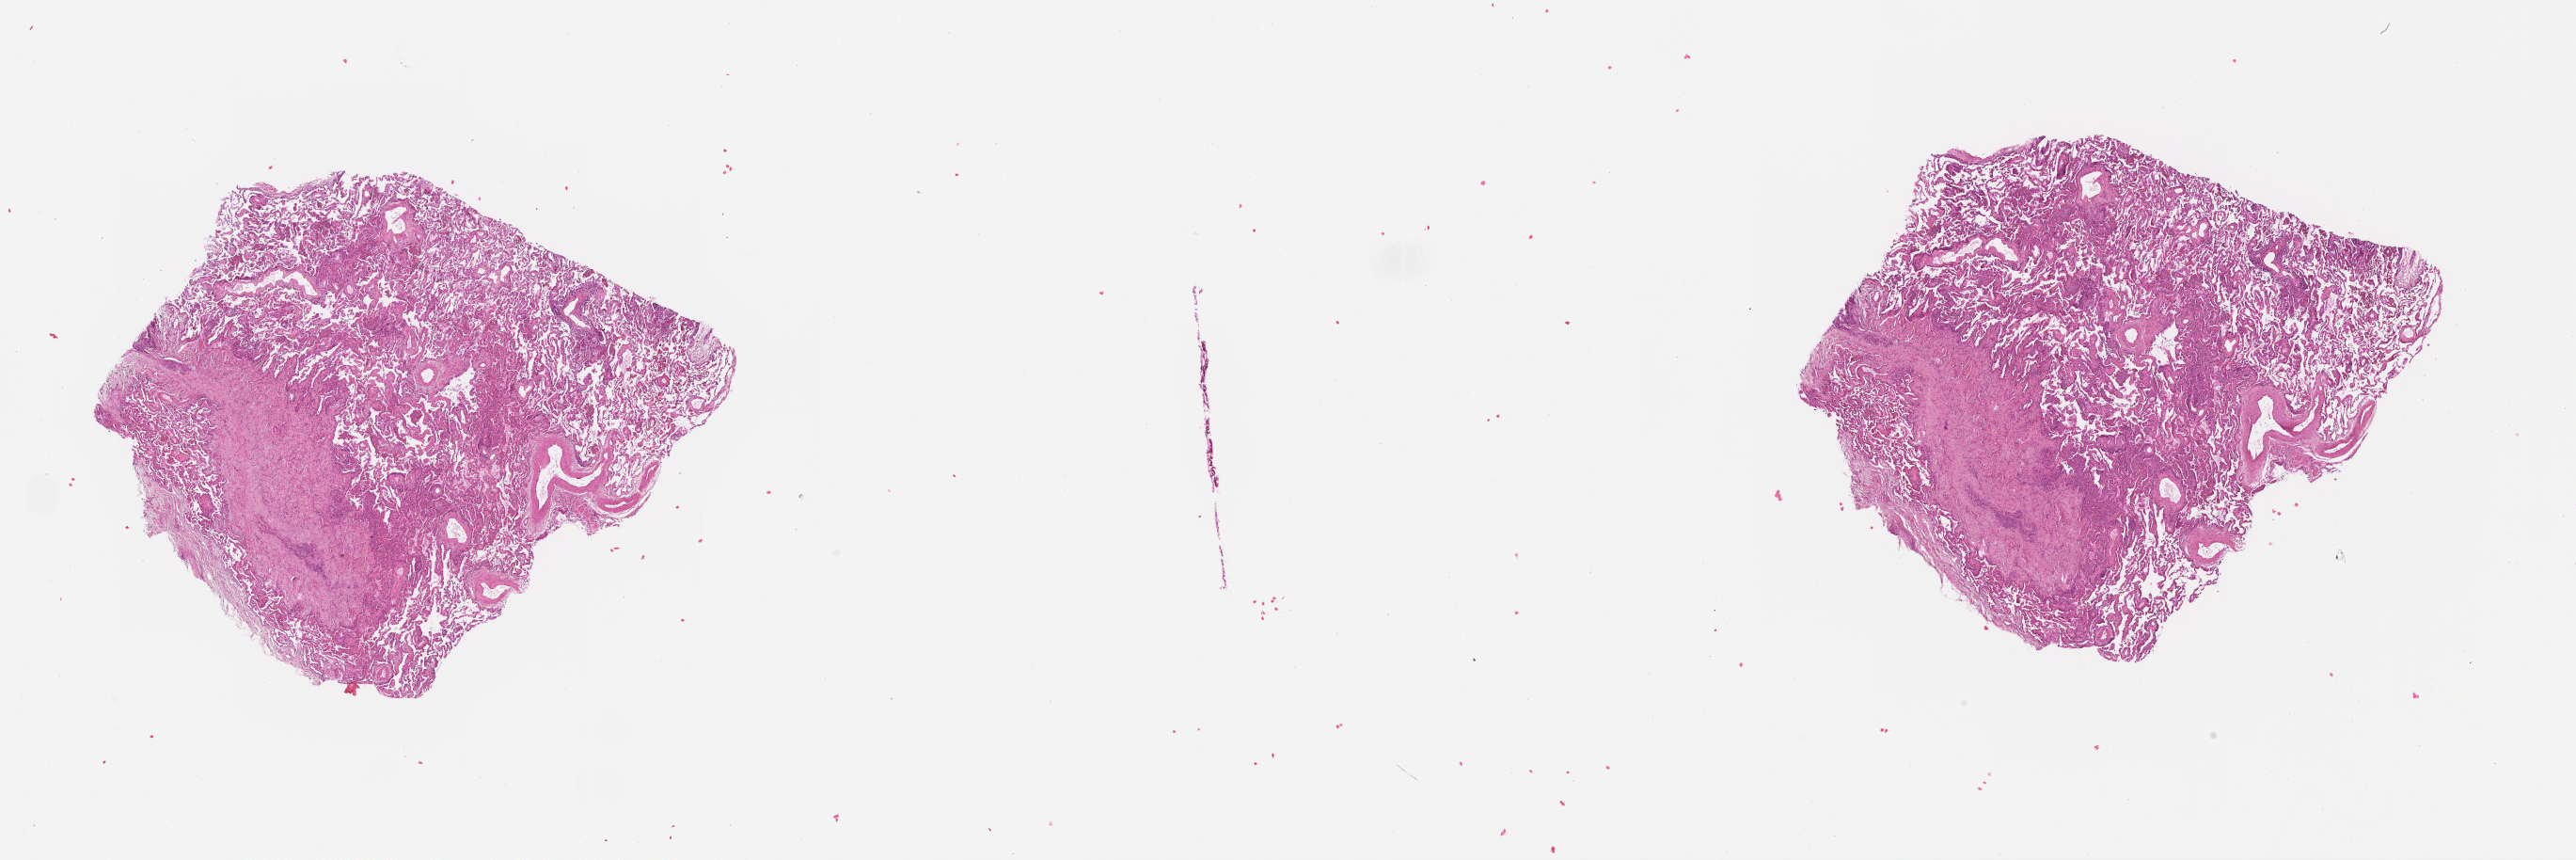
H&E-stained whole-slide image, low-resolution overview of the scanned area, about 22.0 x 7.4 mm (acquisition: 20x scan), lung, tissue type not recorded.
Patient diagnosis (cohort enrolment): squamous cell carcinoma (lung).